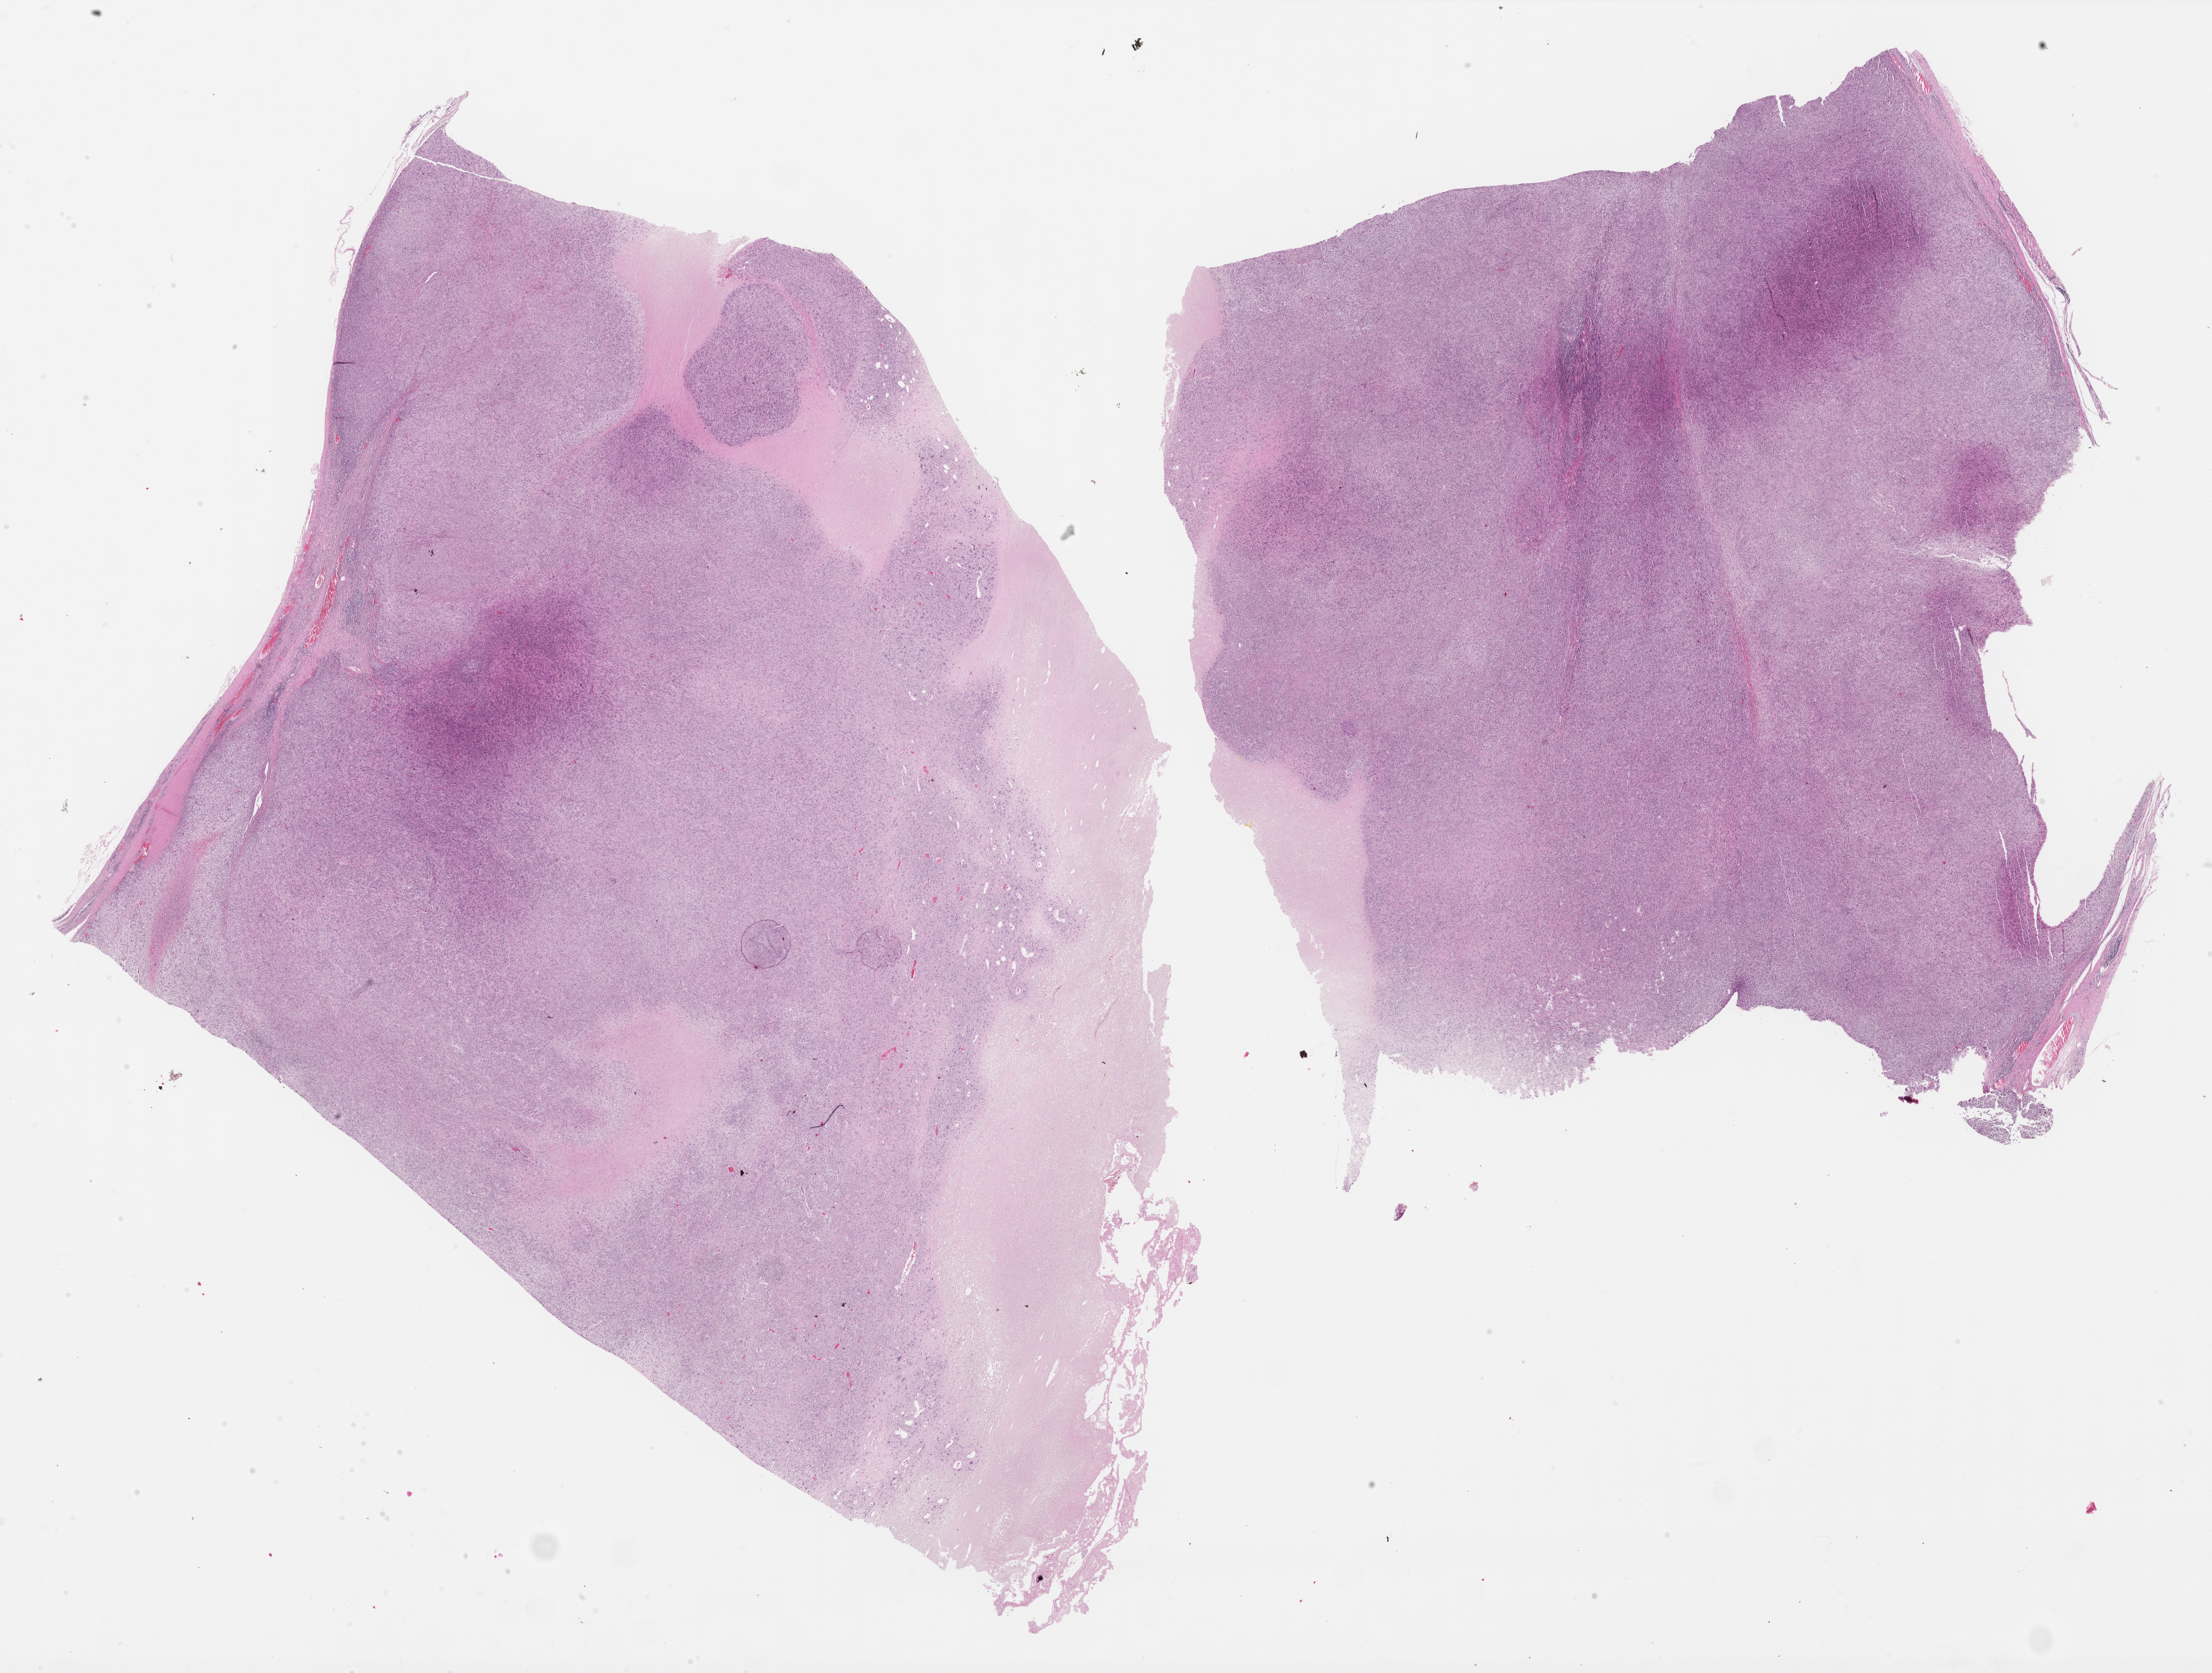
Whole-slide histology image, H&E — shown as a low-resolution overview of the whole scanned area (about 28.5 x 21.6 mm, slide scanned at 40x). FFPE section. Connective, subcutaneous and other soft tissues, primary tumour sample. Male, age 85 years at initial diagnosis.
Histologic diagnosis: Malignant fibrous histiocytoma (connective, subcutaneous and other soft tissues of lower limb and hip).